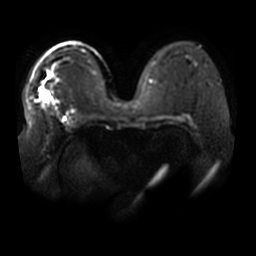
Breast MRI, one axial slice; position 28 of 44 along the scan axis; diffusion-weighted series; image 2 of 4 stored at this slice position (different b-values; order by instance number); 3 T; 256 × 256 image matrix. Female patient.
Annotated regions visible in this slice (manually delineated by an expert):
- tumour on diffusion-weighted imaging: box from (x=39, y=87) to (x=50, y=102) px